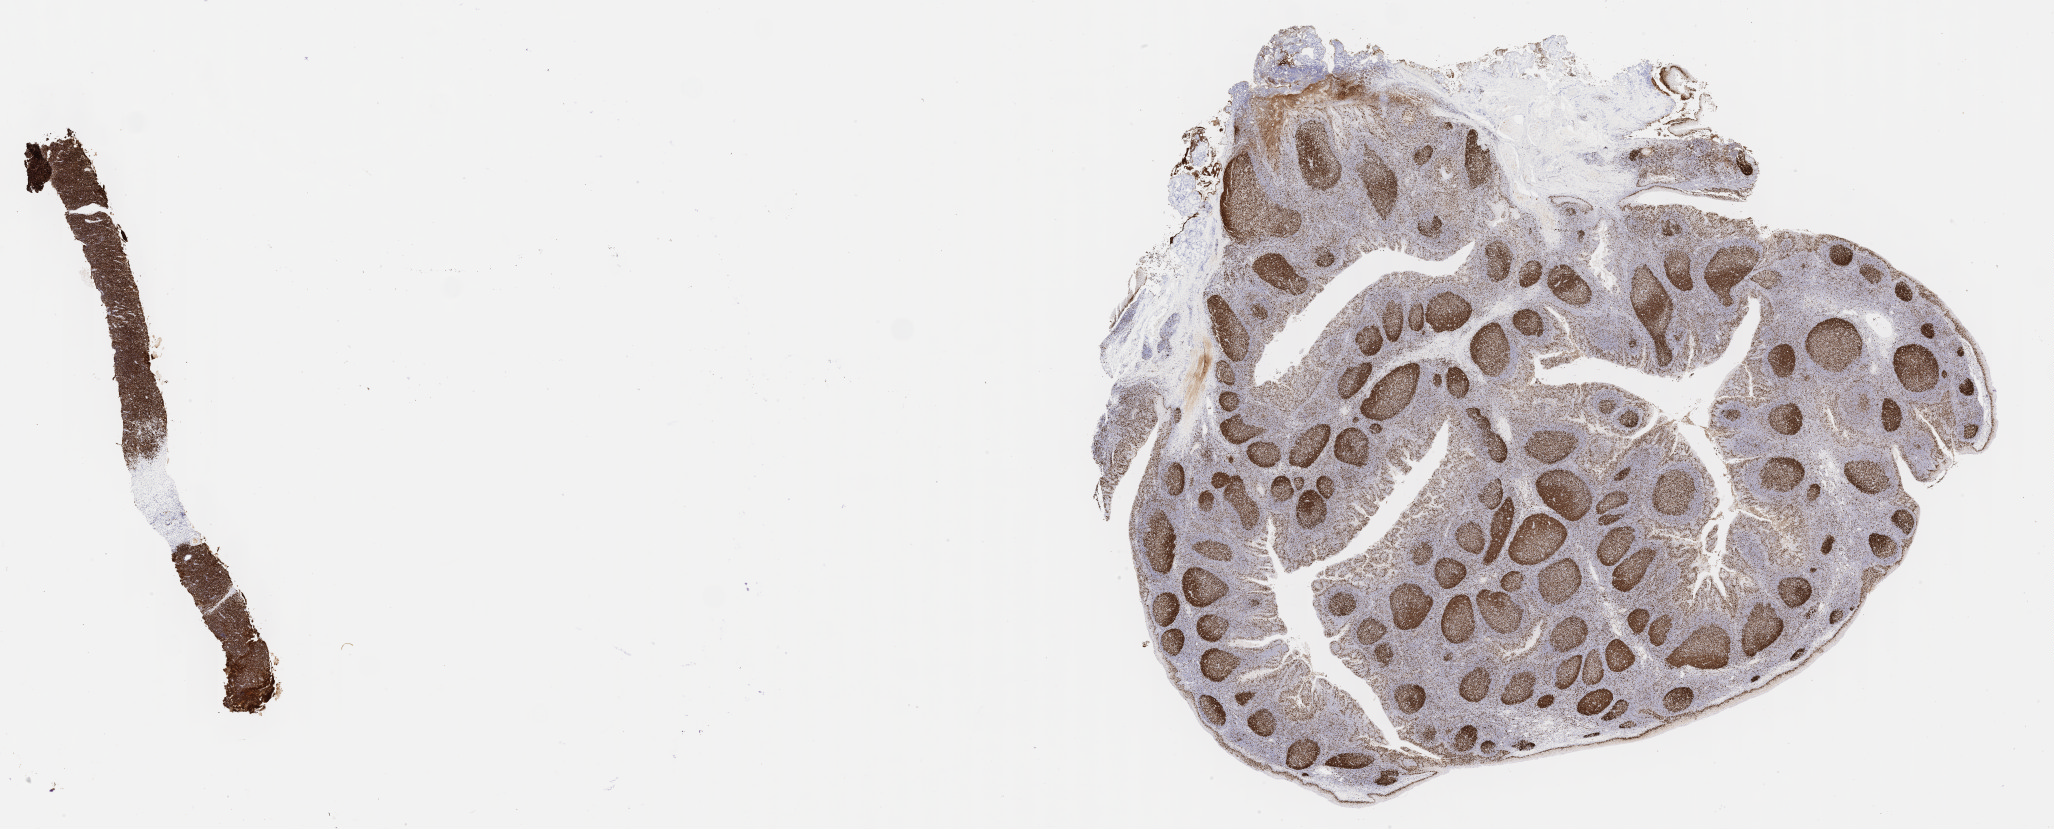
IHC for Ki-67, whole-slide image, whole scanned area (about 33.2 x 13.4 mm) shown as a low-resolution overview. Specimen: tumor tissue. Male patient; age at initial diagnosis 7 years.
Histologic diagnosis: Neoplasm, uncertain whether benign or malignant.